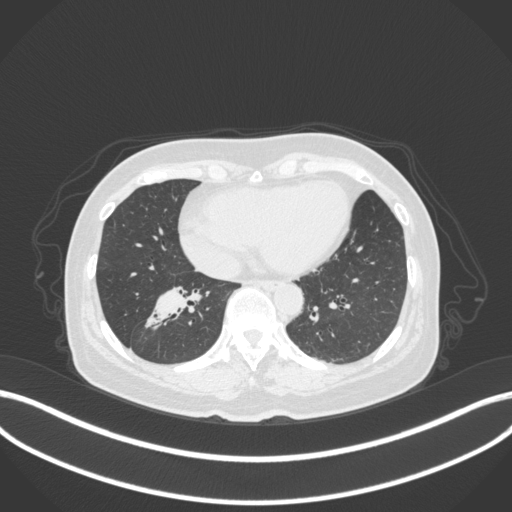
Chest CT, one axial slice; slice 134 of 429 in the series (ordered by position); reconstruction kernel B31f; 120 kVp; lung window (W 1500 / L -600 HU); 512 × 512 image matrix, field of view 400 × 400 mm. Female patient, age 67 years. Case-level facts recorded for this patient, not image findings: clinical TNM (as recorded): T1c N1 M0.
Annotated regions visible in this slice (bounding box drawn by a radiologist):
- lung tumour (recorded histology: adenocarcinoma): box from (x=146, y=278) to (x=212, y=336) px